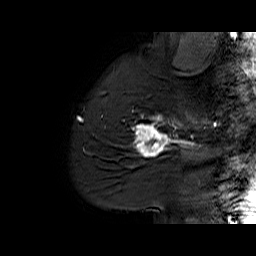
Breast MRI (dynamic contrast-enhanced), one sagittal slice. Slice 49 of 60 in the series (ordered by position). Dynamic contrast-enhanced series, time point 2 of 6 at this slice position (early post-contrast). 1.5 T. TE 6.1 ms, TR 32.9 ms. 256 × 256 image matrix. Female patient. Case-level facts recorded for this patient, not image findings: setting: breast cancer imaged before/during neoadjuvant chemotherapy; receptor status: HER2-positive.
Annotated regions visible in this slice (semi-automatic segmentation, software-assisted and operator-edited):
- analysis volume of interest (the breast-tissue region the enhancement analysis was run in; not a lesion): box from (x=127, y=95) to (x=194, y=165) px
- tumour enhancement mask (voxels above the 100 % enhancement threshold inside the analysis volume of interest): (x=133, y=114)–(x=194, y=157)